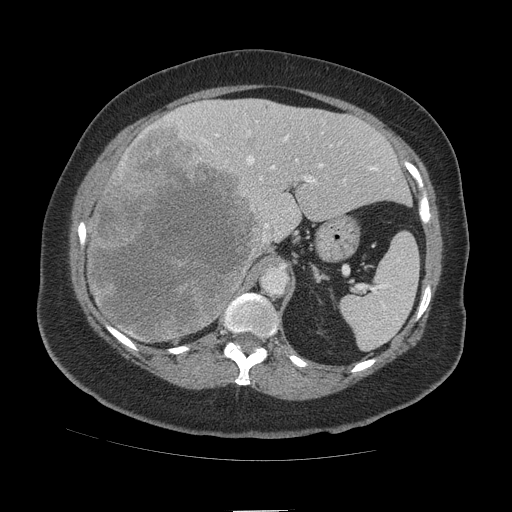
Contrast-enhanced abdominal CT (liver protocol), one axial slice. Reconstruction kernel STANDARD. Soft-tissue window (W 400 / L 40 HU). 2.5 mm slice thickness. 512 × 512 image matrix. From the clinical record (not read from this slice): diagnosis: hepatocellular carcinoma (patient treated with transarterial chemoembolisation; whether this scan precedes or follows treatment is not stated here); TNM stage (as recorded): Stage-IVB; Child-Pugh class: A.
Outlined on this slice (semi-automatic segmentation, software-assisted and operator-edited):
- liver parenchyma outside the tumour (the mass and vessels are separate outlines, so this box may not span the whole liver): box from (x=88, y=98) to (x=410, y=336) px
- mass: (x=89, y=120)–(x=266, y=344)
- liver vessels: (x=166, y=114)–(x=393, y=234)